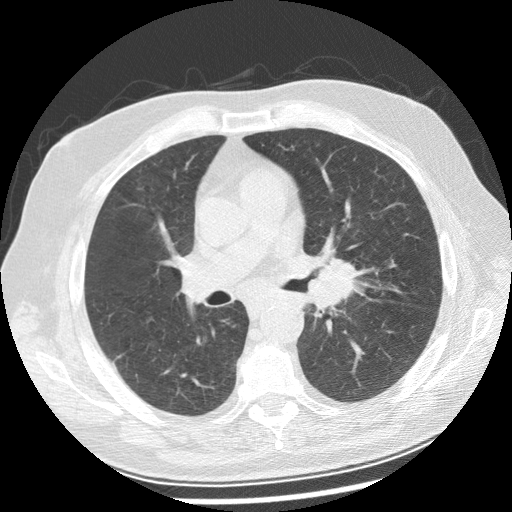
Low-dose screening chest CT, one axial slice; position 143 of 250 along the scan axis; reconstruction kernel STANDARD; lung window (W 1500 / L -600 HU); 2.5 mm slice thickness; 512 × 512 image matrix, field of view 360 × 360 mm.
Outlined on this slice (outlined manually by an expert reader):
- lesion 1 (tumor, left main bronchus): box from (x=308, y=257) to (x=356, y=308) px